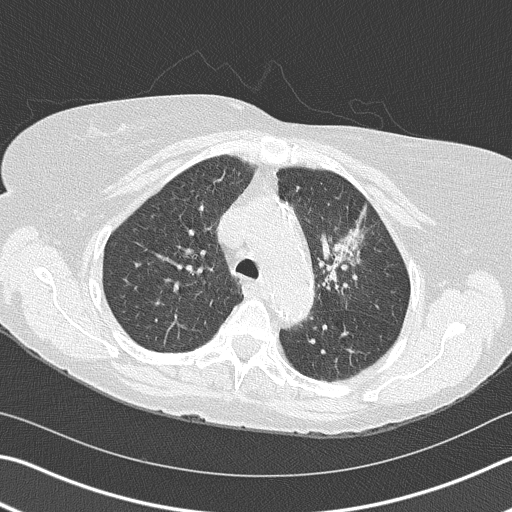
Axial slice from a low-dose chest CT screening exam, second annual screen, lung window (W 1500 / L -600 HU), 120 kVp, slice 115 of 153 in the series. Female, age 68 years at enrolment.
- Expert reader's lesion annotation, bounding box [x1, y1, x2, y2] px = [293, 199, 390, 311].
- The exam's reader record, not a measurement of the box and not confirmed to be the same lesion: non-calcified nodule or mass ≥4 mm, left upper lobe, 4 × 2 mm, spiculated (stellate) margins, soft tissue attenuation, pre-existing on the prior screen: yes; interval growth: yes.
- Lung cancer was diagnosed 392 days after this screen (after the third annual screen): adenocarcinoma, NOS, left upper lobe, poorly differentiated (G3), stage IB (AJCC 6th edition), 50 mm at pathology.